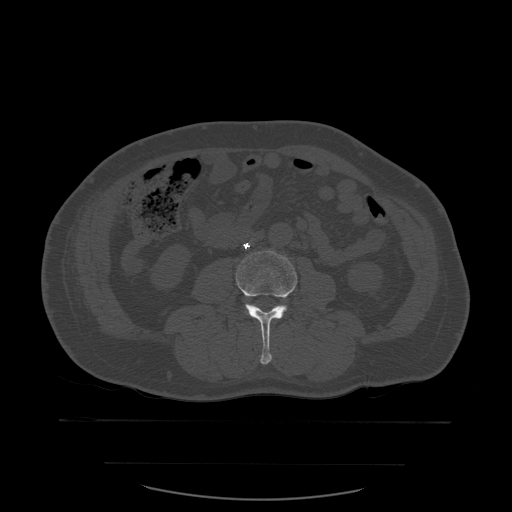
CT including the spine, one axial slice. Position 189 of 590 along the scan axis. Bone window (W 1800 / L 400 HU). 512 × 512 image matrix, field of view 479 × 479 mm. Patient age 71 years. From the clinical record (not read from this slice): primary cancer: lung; vertebrae with lytic lesions (as recorded): T1, T2, L5, S1.
Structures marked on this image (semi-automatic segmentation, software-assisted and operator-edited):
- L3 vertebra: bounding box <236,251,298,365> (left, top, right, bottom; pixels)